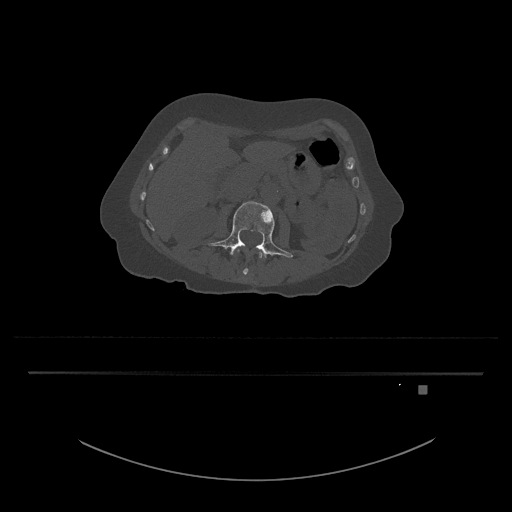
CT including the spine, one axial slice; position 438 of 797 along the scan axis; 120 kVp; bone window (W 1800 / L 400 HU); 0.5 mm slice thickness; 512 × 512 image matrix, field of view 500 × 500 mm. Female patient, age 57 years. From the clinical record (not read from this slice): primary cancer: cervical.
Structures marked on this image (semi-automatically segmented with operator editing):
- L3 vertebra: bounding box [x1, y1, x2, y2] px = [208, 201, 293, 258]